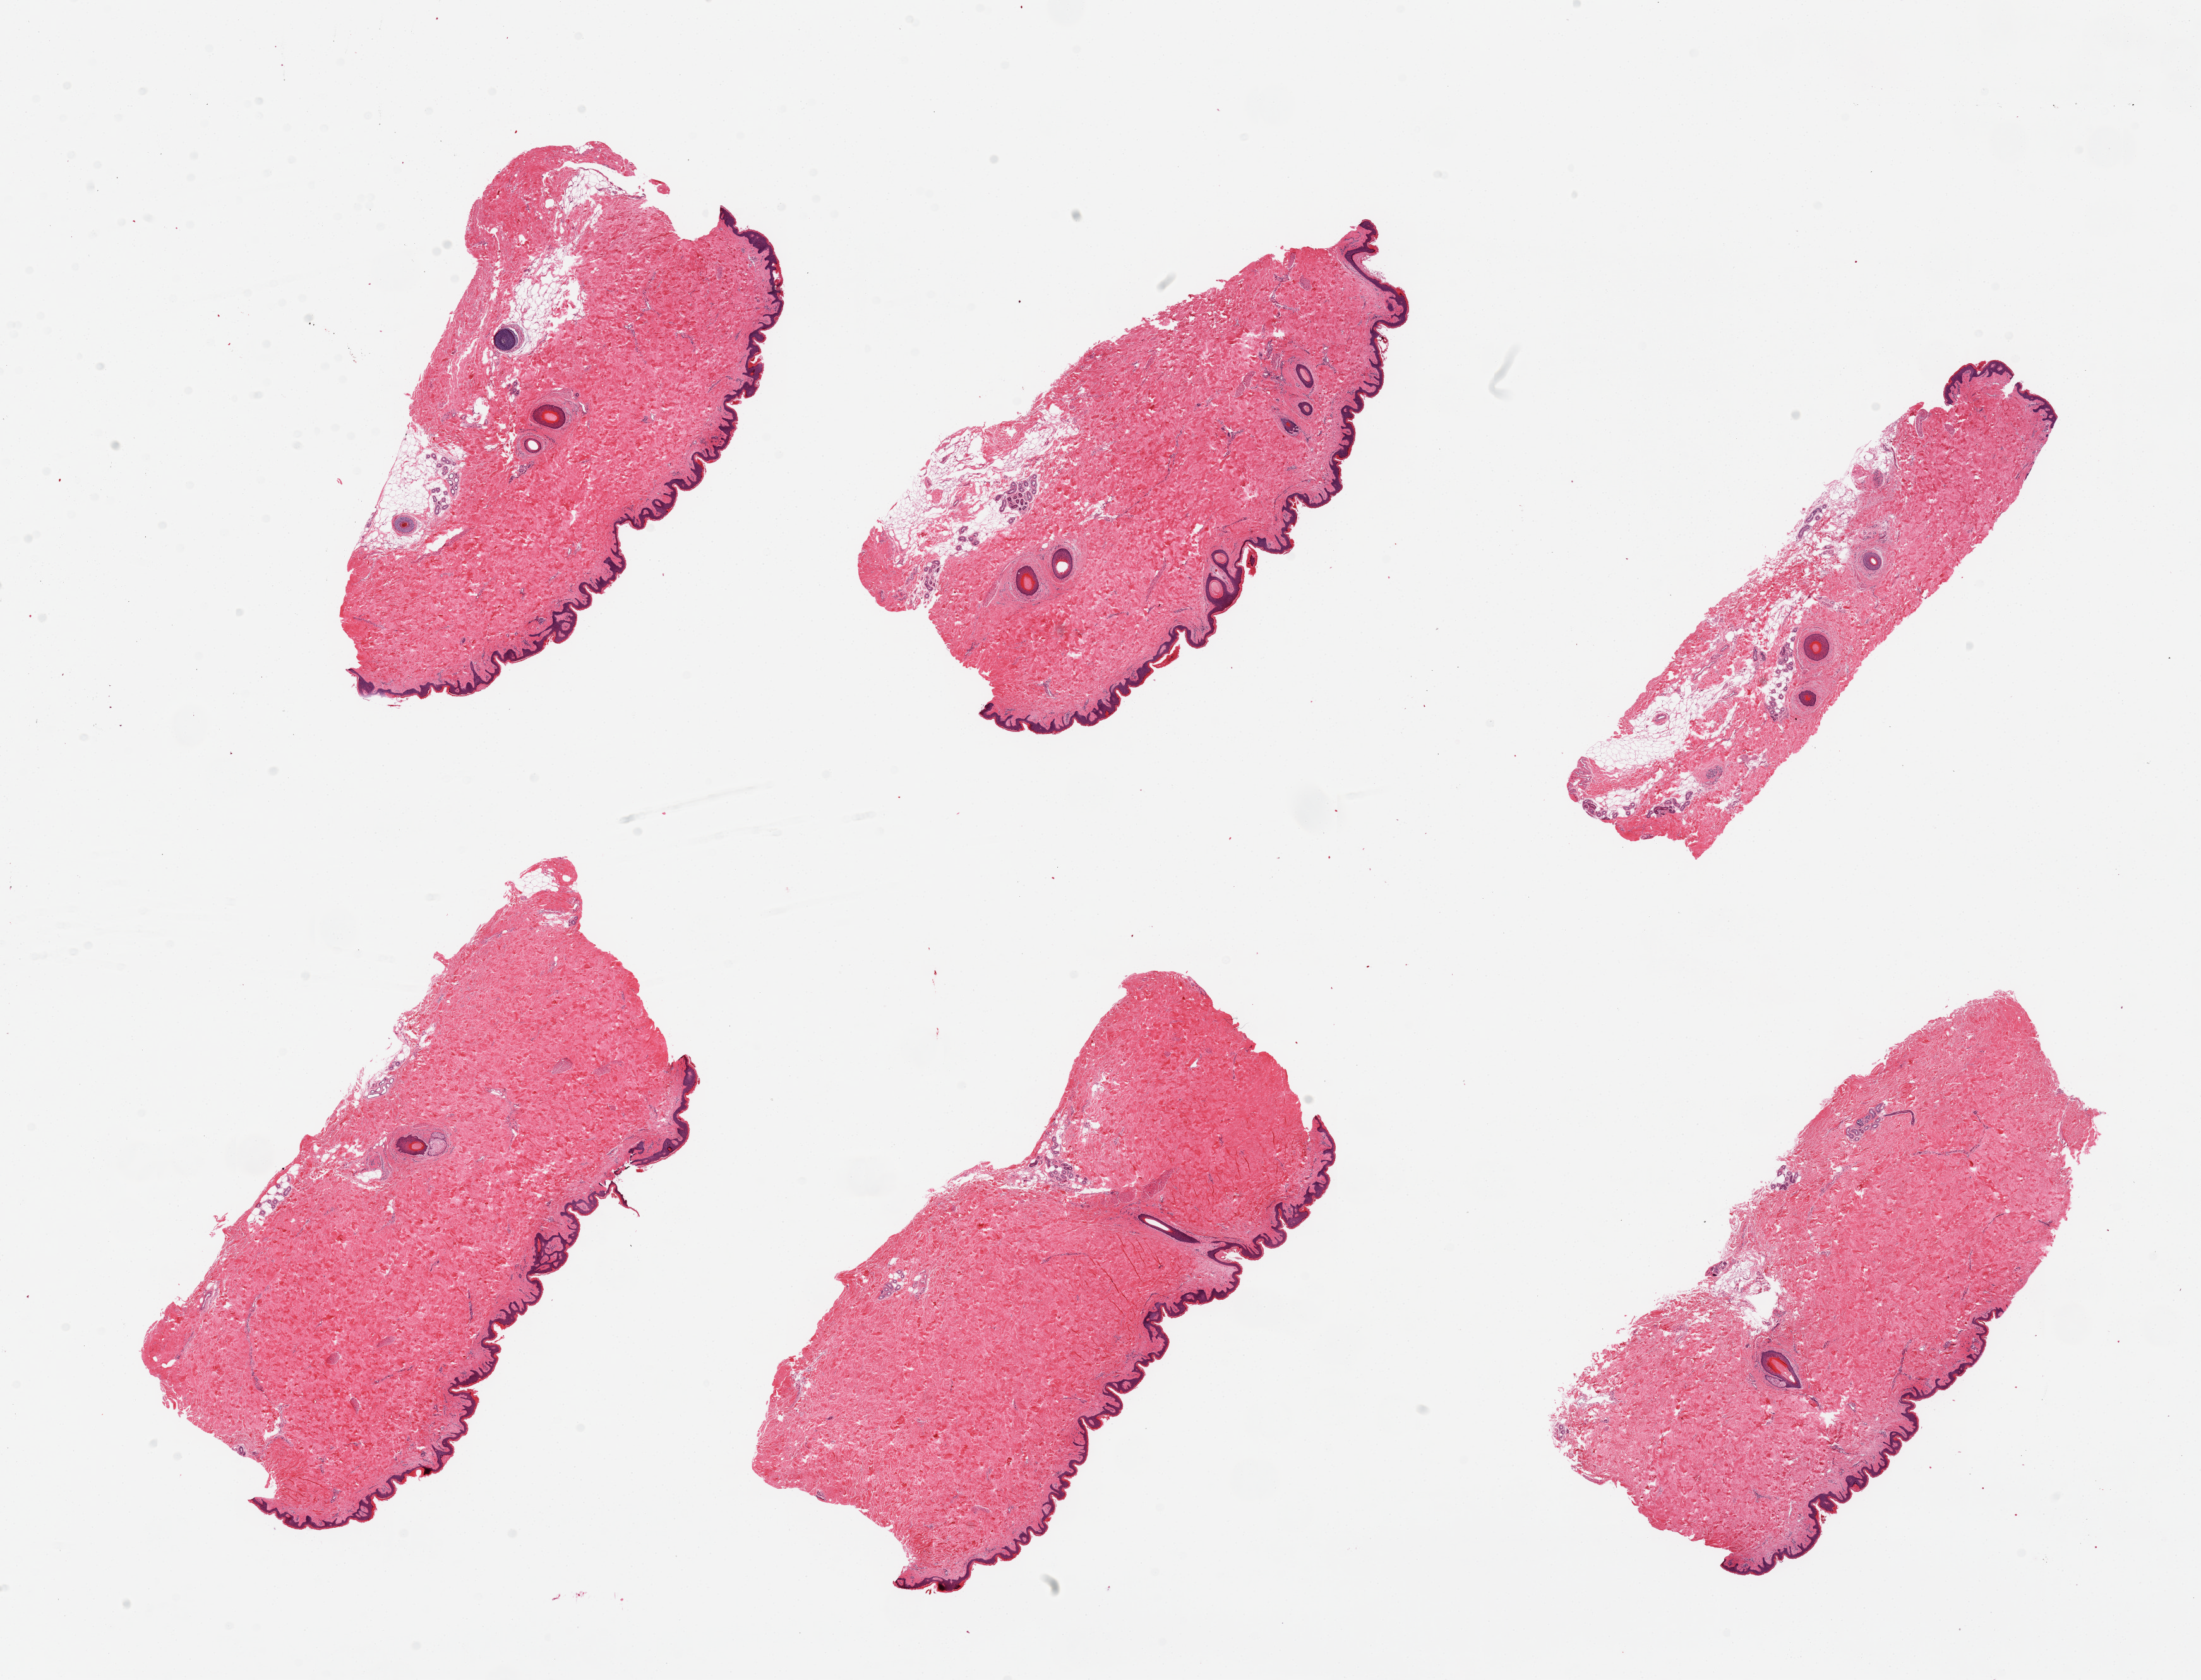
Digitized haematoxylin and eosin-stained section — whole scanned area (about 27.6 x 21.0 mm) shown as a low-resolution overview. PAXgene-fixed, paraffin-embedded tissue. Target tissue: skin of suprapubic region. Tissue donor sample. Donor sex: male.
Review note (as recorded): 6 pieces, minimal dermal fat, squamous epithelium is ~50-60 microns.